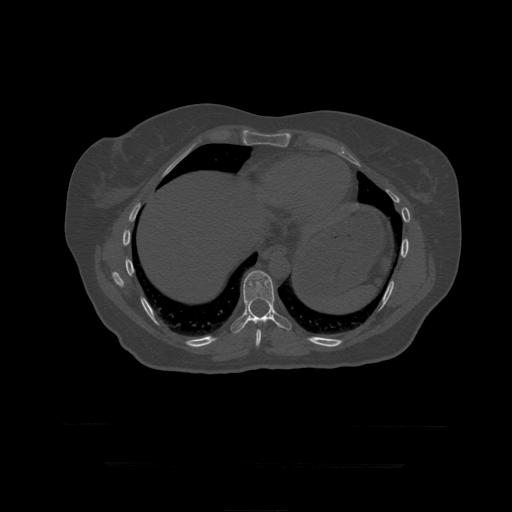
CT including the spine, one axial slice; slice 246 of 399 in the series (ordered by position); 120 kVp; bone window (W 1800 / L 400 HU); 1.25 mm slice thickness; 512 × 512 image matrix. Patient age 41 years. Case-level facts recorded for this patient, not image findings: primary cancer: breast.
Structures marked on this image (semi-automatically segmented with operator editing):
- T10 vertebra: box from (x=231, y=271) to (x=292, y=334) px
- T9 vertebra: (x=256, y=329)–(x=262, y=346)